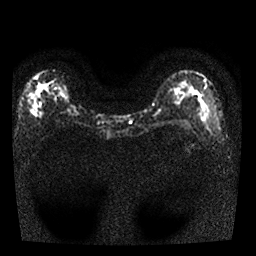
Breast MRI, one axial slice; position 12 of 25 along the scan axis; diffusion-weighted series; image 2 of 4 stored at this slice position (different b-values; order by instance number); 1.5 T; 4 mm slice thickness; 256 × 256 image matrix. Female patient.
Structures marked on this image (outlined manually by an expert reader):
- tumour on diffusion-weighted imaging: bounding box (x1, y1, x2, y2) in pixels: (37, 83, 48, 93)